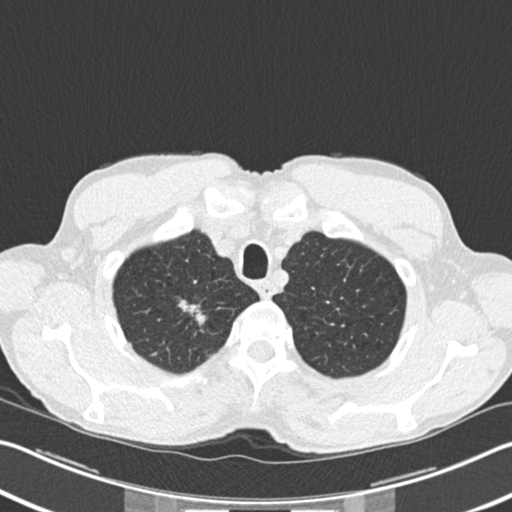
Low-dose screening chest CT, axial slice. Second annual screen. Lung window (W 1500 / L -600 HU). 2 mm slice thickness. Standard (soft-tissue) reconstruction kernel (B30f). 120 kVp. Slice 29 of 220 in the series. Male, age 62 years at enrolment. Former smoker at enrolment.
Expert-annotated lung lesion, box from (x=171, y=293) to (x=213, y=339) px. The screening reader recorded 2 non-calcified nodules or masses ≥4 mm on this exam (right upper lobe, right upper lobe); which of them this box marks is not recorded.